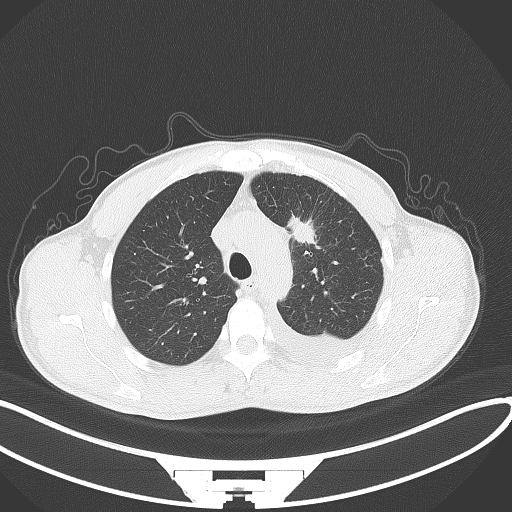
Chest CT, one axial slice; position 97 of 130 along the scan axis; reconstruction kernel B70f; 120 kVp; lung window (W 1500 / L -600 HU); 512 × 512 image matrix. Patient: male, 49 years. Case-level facts recorded for this patient, not image findings: clinical TNM (as recorded): T1c N1 M1.
Outlined on this slice (rectangle marked by the reading radiologist):
- lung tumour (recorded histology: adenocarcinoma): bounding box [x1, y1, x2, y2] px = [285, 205, 317, 251]